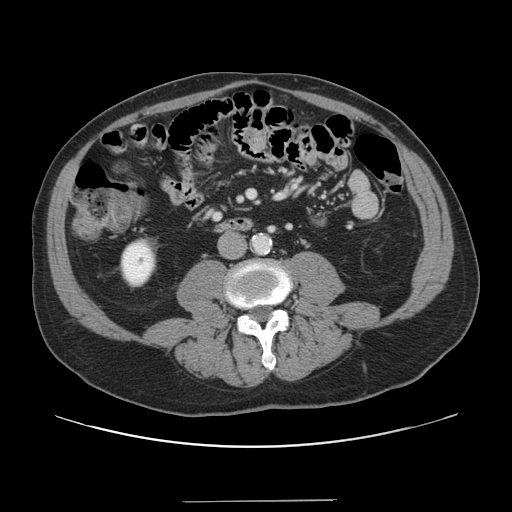
Contrast-enhanced abdominal CT, one axial slice; slice 18 of 151 in the series (ordered by position); 120 kVp; intravenous contrast given; soft-tissue window (W 400 / L 40 HU); 512 × 512 image matrix, field of view 399 × 399 mm. Male patient, age 63 years. Case-level facts recorded for this patient, not image findings: diagnosis: colorectal cancer liver metastases, imaged before liver resection; multiple liver metastases: no; largest metastasis: 2.1 cm; disease in both lobes: no.
Outlined on this slice (manually delineated by an expert):
- portal vein (with intrahepatic branches): box from (x=249, y=191) to (x=253, y=197) px